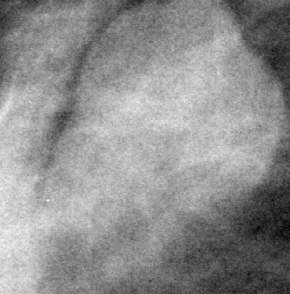
Cropped region of a digitized screen-film mammogram centred on a radiologist-marked abnormality; right breast; MLO view.
- Finding: mass, shape oval, margins circumscribed; BI-RADS assessment category 4; pathology result (as recorded, not read from the image): benign.